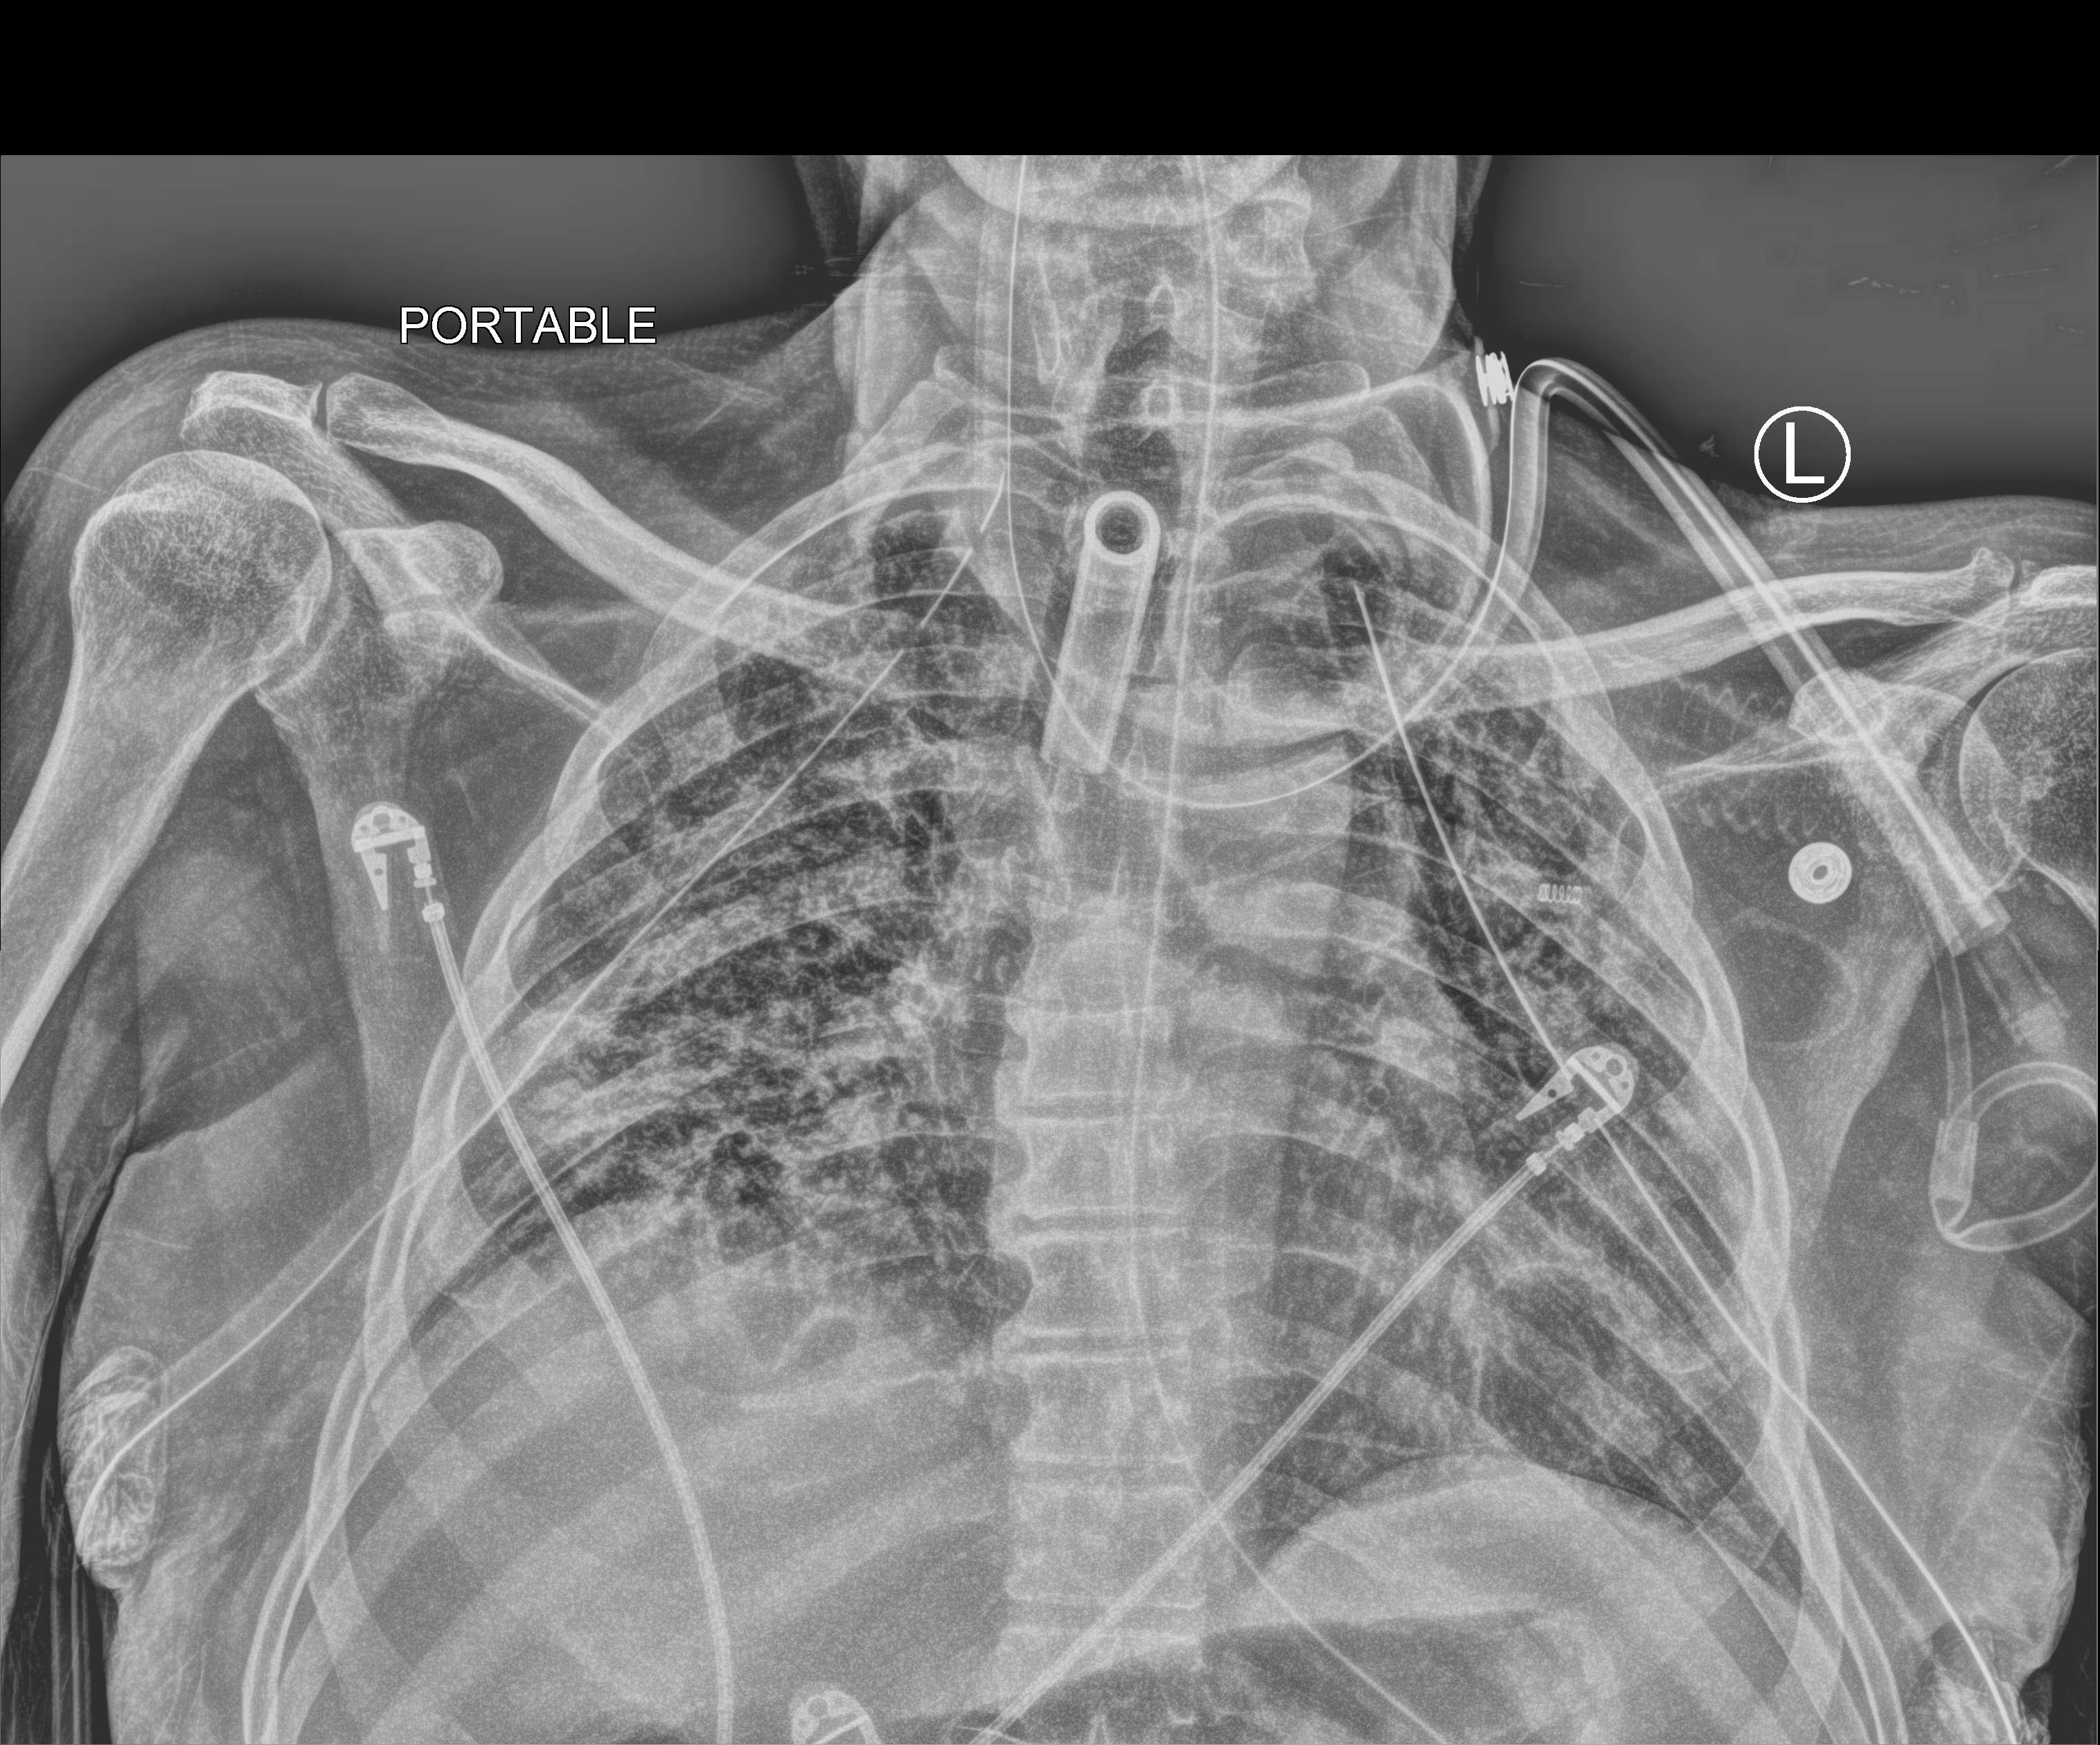
Chest X-ray (portable); anteroposterior (AP) projection. Patient hospitalised with COVID-19; male, aged 18–59 years.
Admission-level facts for this patient (not findings on this image; timing relative to this image not recorded): admitted to intensive care during this hospital stay: yes; mechanically ventilated during this hospital stay: yes; other chronic lung disease (admission record): no.